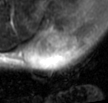
MRI of an extremity soft-tissue mass, one axial slice; position 28 of 42 along the scan axis; T2-weighted fat-saturated; MR volume resampled by the dataset authors to the PET/CT grid (not the native acquisition matrix); 3.27 mm slice thickness; 108 × 103 image matrix. Male patient. Case-level facts recorded for this patient, not image findings: histological type: leiomyosarcoma; grade: intermediate; site of the primary tumour: left pelvis.
Annotated regions visible in this slice (expert contour drawn on MRI and transferred to this co-registered scan by the dataset authors):
- gross tumour volume (mass): box from (x=23, y=23) to (x=84, y=70) px